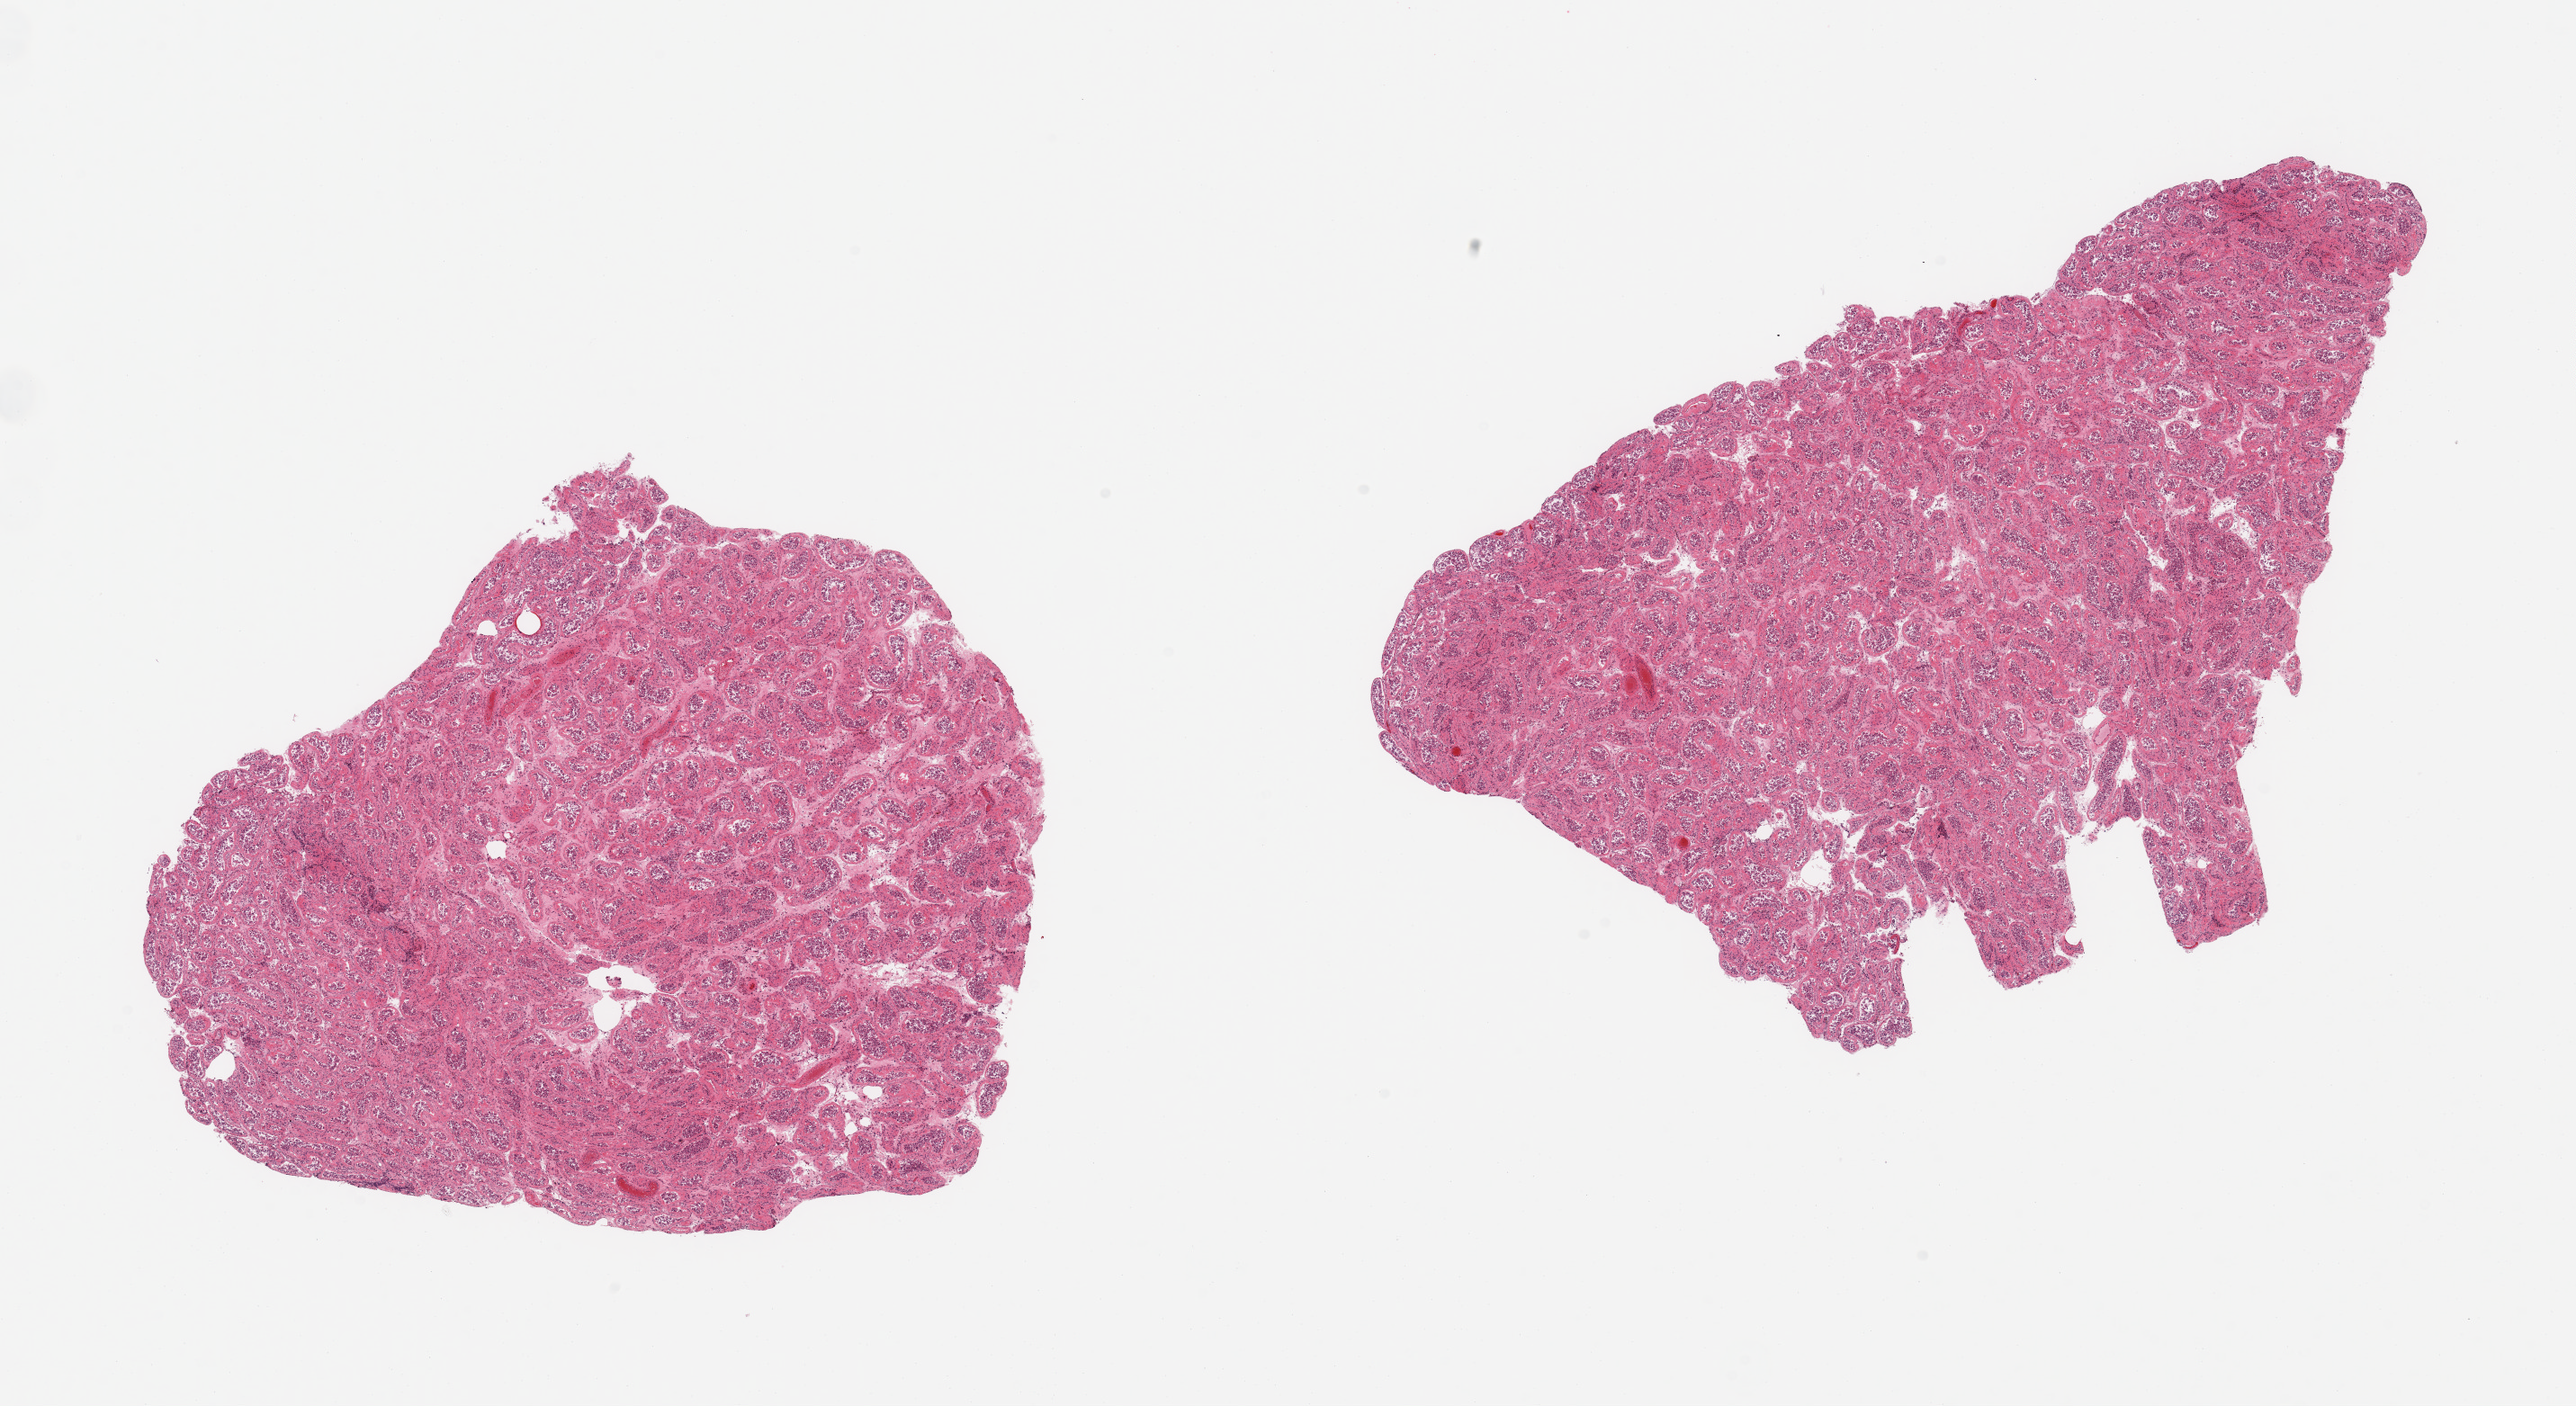
Digitized haematoxylin and eosin-stained section — a low-resolution overview of the entire scanned area, about 22.6 x 12.4 mm; PAXgene-fixed paraffin-embedded (PFPE) section; sampled site (target tissue): testis; tissue donor sample.
Reviewer comment on this tissue sample: 2 pieces; thickening of tubular basement membrane; absence of speramtogenesis.